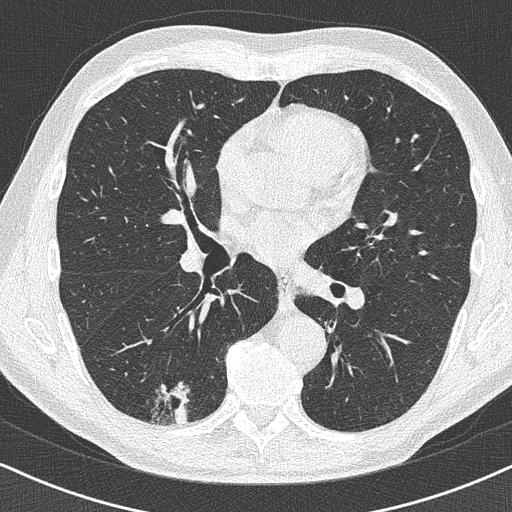
Low-dose screening chest CT, axial slice, baseline screening round, lung window (W 1500 / L -600 HU), 1 mm slice thickness, lung (sharp) reconstruction kernel (B50f), slice 212 of 438 in the series. Male, age 63 years at enrolment. Former smoker at enrolment.
Lesion marked by an expert reader, bounding box [x1, y1, x2, y2] px = [136, 369, 207, 429]. Screening reader's record for this exam (one nodule recorded; not confirmed to be the boxed lesion): non-calcified nodule or mass ≥4 mm, right lower lobe, 16 × 13 mm, poorly defined margins. Lung cancer was diagnosed 74 days after this screen: adenocarcinoma, NOS, right lower lobe, moderately differentiated (G2), stage IA (AJCC 6th edition), 20 mm at pathology.